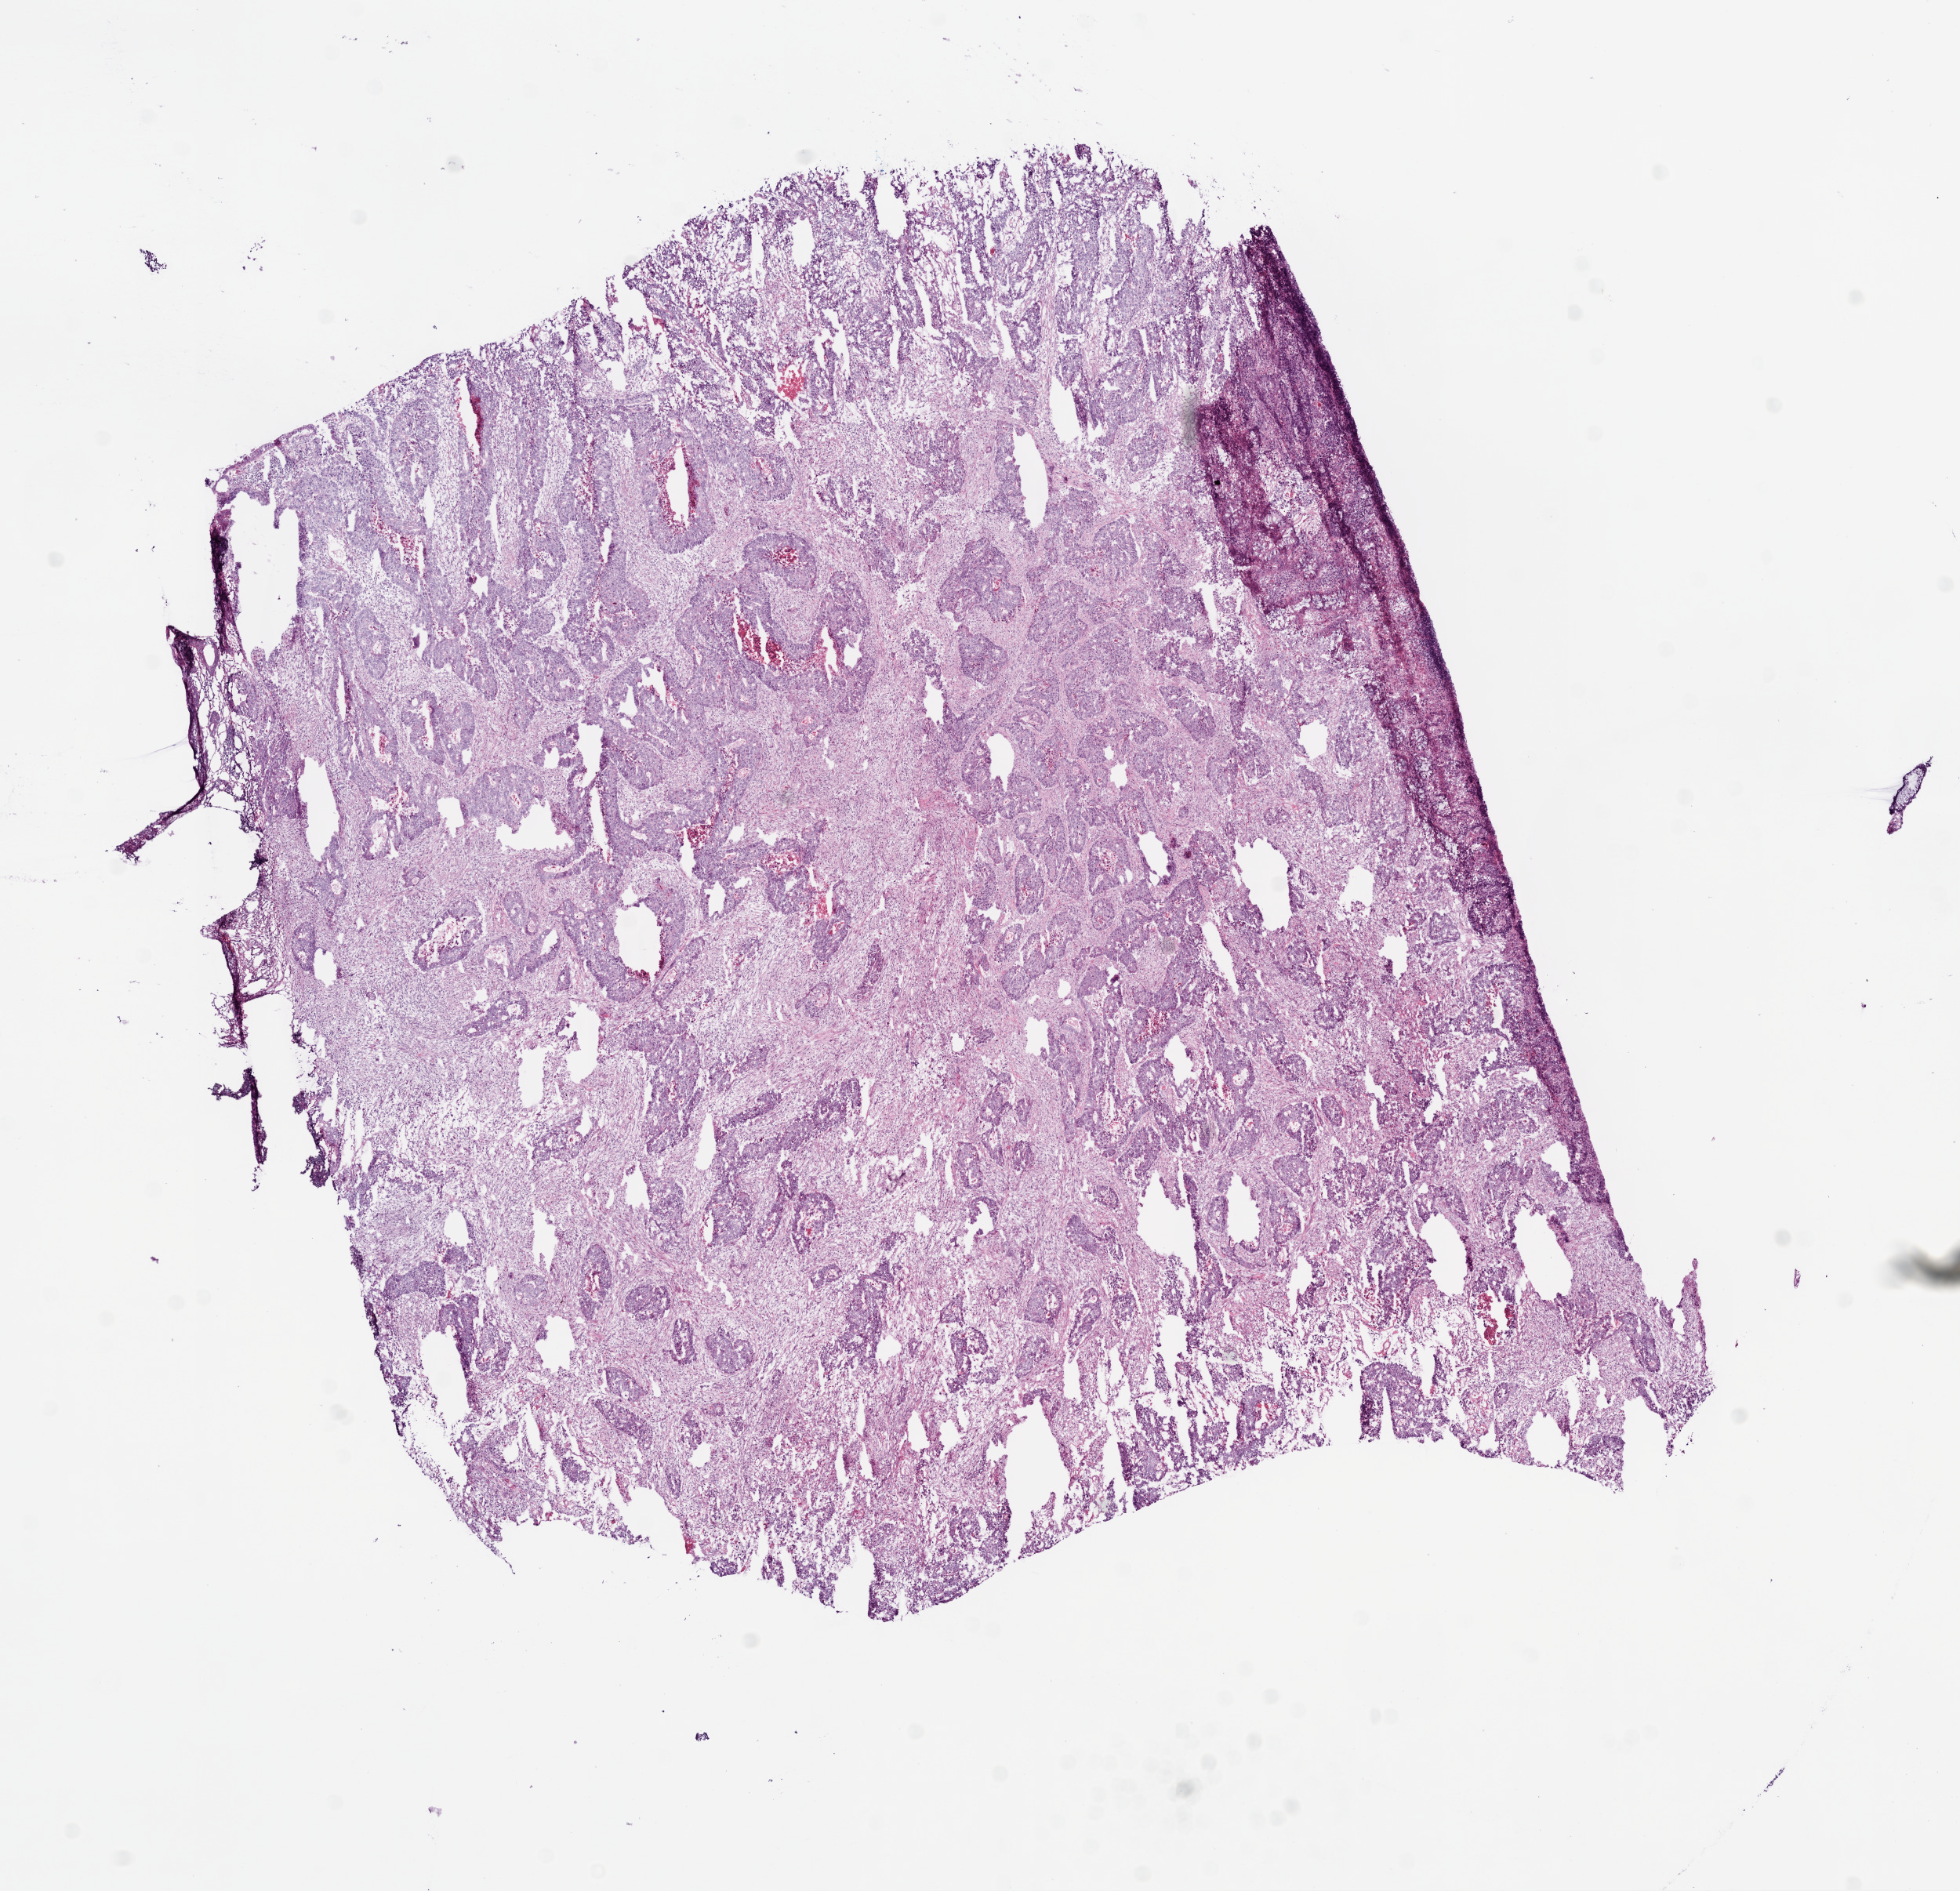
Hematoxylin and eosin (H&E) stained whole-slide image, a low-resolution overview of the entire scanned area, about 10.0 x 9.7 mm (slide scanned at 20x), frozen section, rectum, primary tumour sample. Patient: male, age at initial diagnosis 69 years. Slide review estimates, as recorded: tumour cells 55%, tumour nuclei 70%.
Pathologic diagnosis: Adenocarcinoma, NOS.